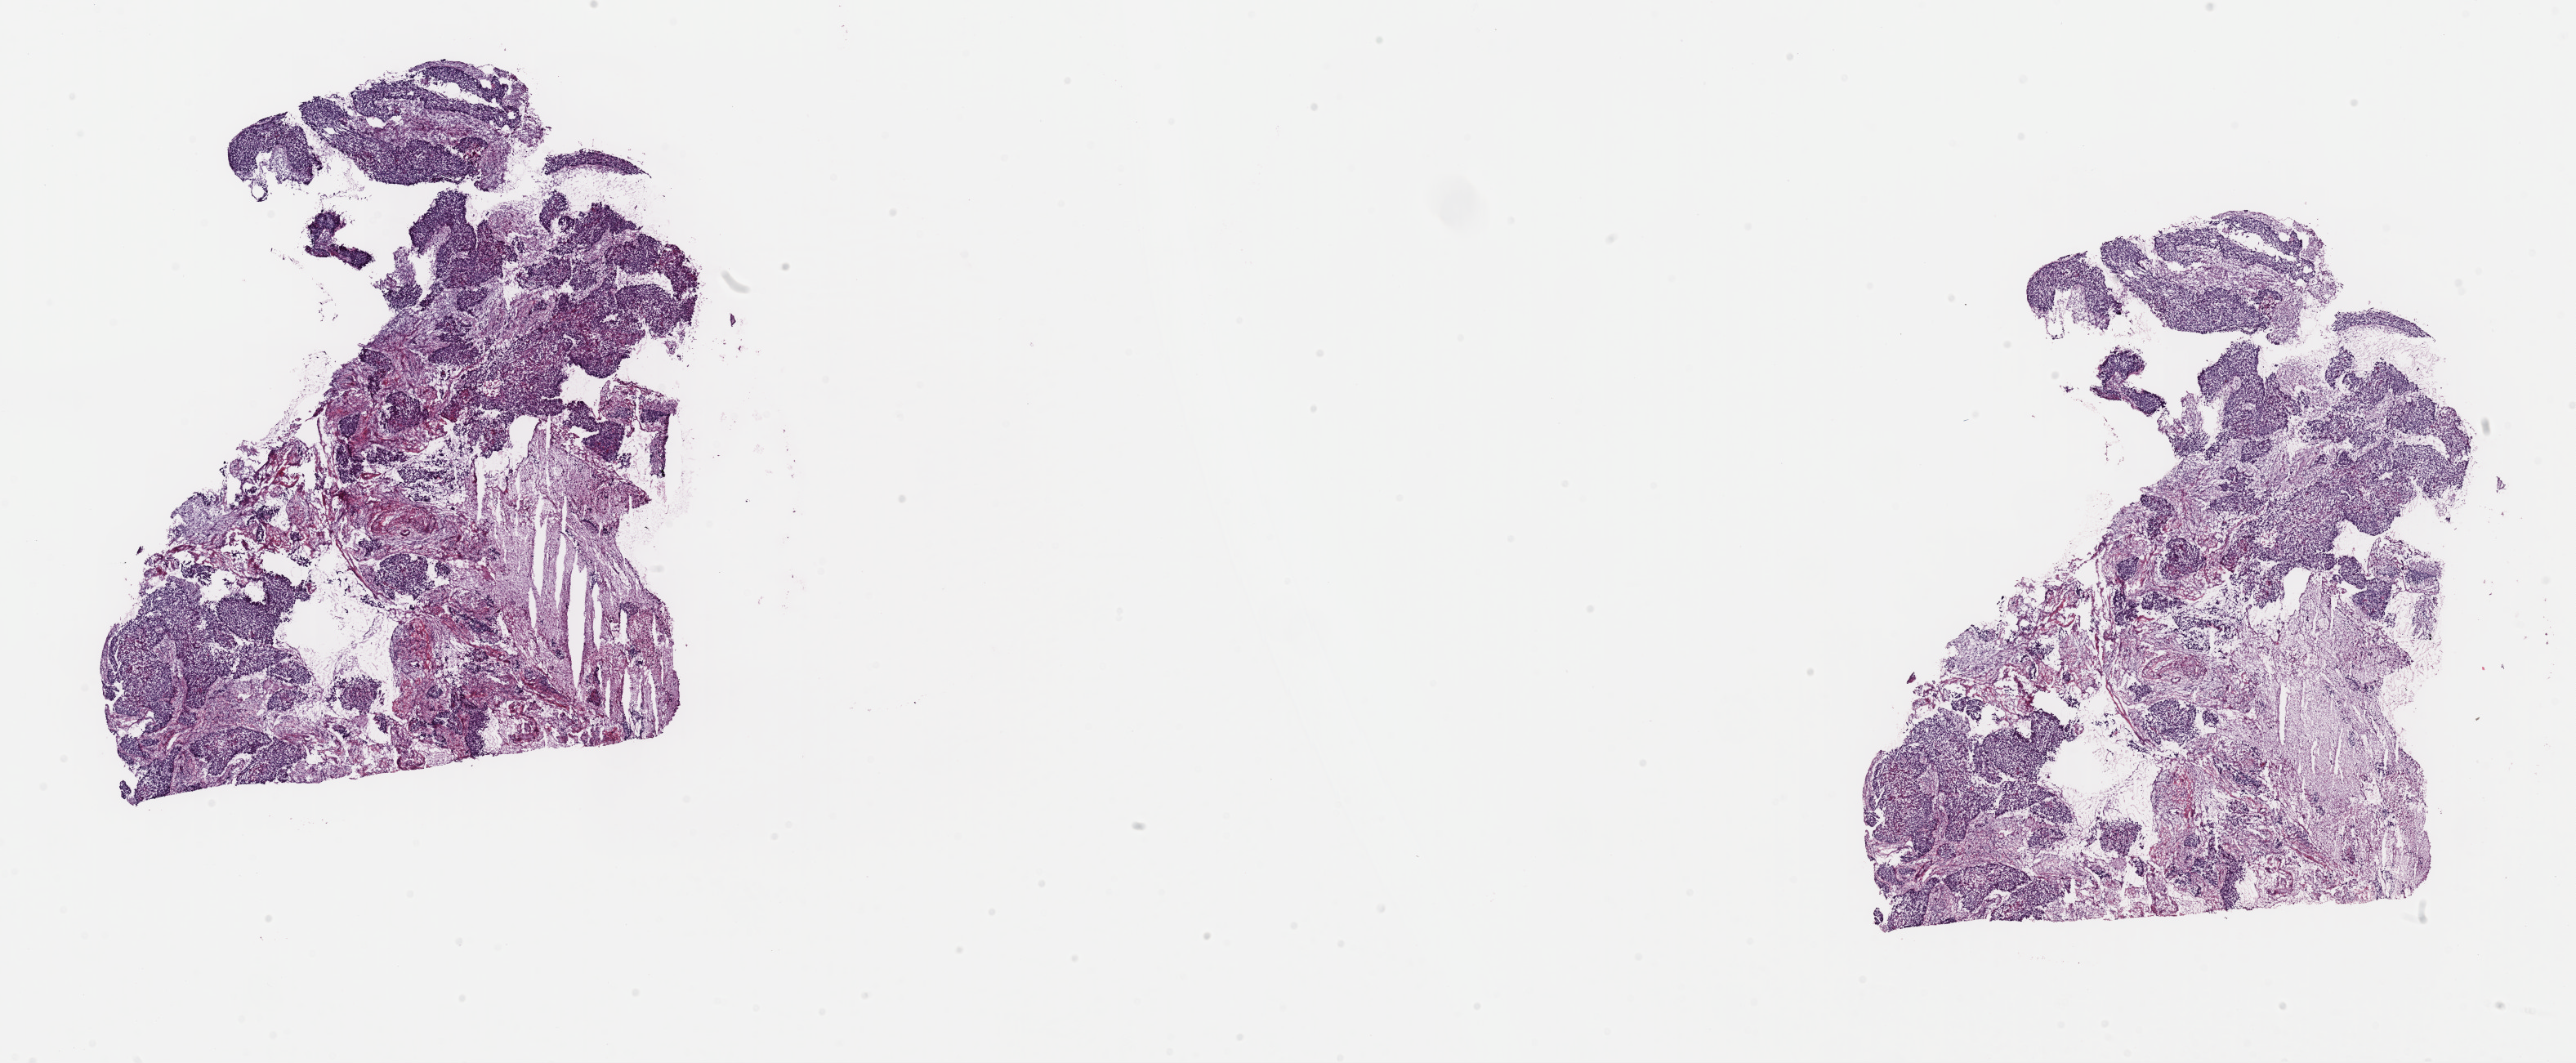
Whole-slide histology image, Hematoxylin and eosin (H&E) stained — a low-resolution overview of the entire scanned area, about 24.9 x 10.3 mm (slide scanned at 40x); frozen section; sample: primary tumour, cervix. Female, age 44 years at initial diagnosis. Histologic grade: G2 (moderately differentiated). Pathologist review of this section (percent, as recorded): tumour cells 50%, tumour nuclei 68%, normal cells 30%, stromal cells 18%, necrosis 2%. Infiltration values recorded for this section: lymphocyte infiltration 10%, monocyte infiltration 0%, neutrophil infiltration 0%.
* FIGO stage: IIIB
* diagnosis: Squamous cell carcinoma, large cell, nonkeratinizing, NOS (cervix uteri)